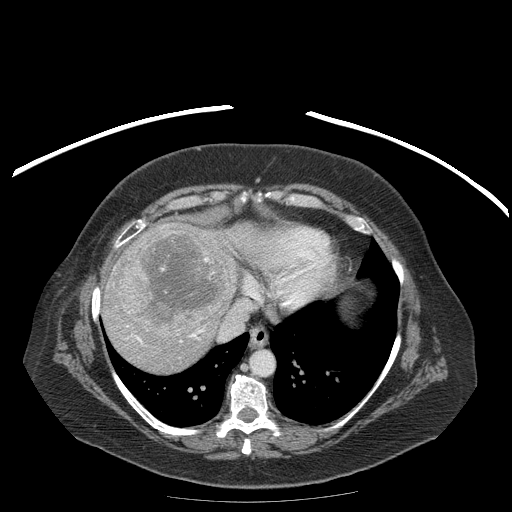
Contrast-enhanced abdominal CT (liver protocol), one axial slice. Position 159 of 204 along the scan axis. Reconstruction kernel STANDARD. Soft-tissue window (W 400 / L 40 HU). 512 × 512 image matrix. Case-level facts recorded for this patient, not image findings: diagnosis: hepatocellular carcinoma (patient treated with transarterial chemoembolisation; whether this scan precedes or follows treatment is not stated here); TNM stage (as recorded): Stage-IIIB; Child-Pugh class: A; tumour differentiation: well differentiated; tumour nodularity: uninodular.
Annotated regions visible in this slice (semi-automatically segmented with operator editing):
- liver parenchyma outside the tumour (the mass and vessels are separate outlines, so this box may not span the whole liver): bounding box [x1, y1, x2, y2] px = [102, 222, 250, 374]
- mass: [118, 229, 230, 336]
- liver vessels: [135, 329, 204, 344]